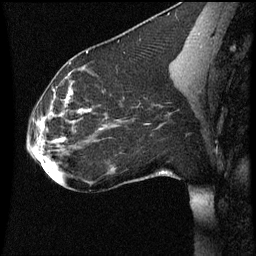
Breast MRI (dynamic contrast-enhanced), one sagittal slice; slice 28 of 60 in the series (ordered by position); dynamic contrast-enhanced series, image 2 of 3 at this slice position (ordered by acquisition); 1.5 T; TE 4.2 ms, TR 8.9 ms; 256 × 256 image matrix, field of view 200 × 200 mm. Female patient, age 35 years. From the clinical record (not read from this slice): setting: breast cancer imaged before/during neoadjuvant chemotherapy; receptor status: HER2-positive.
Annotated regions visible in this slice (semi-automatic segmentation, software-assisted and operator-edited):
- analysis volume of interest (the breast-tissue region the enhancement analysis was run in; not a lesion): bounding box [x1, y1, x2, y2] px = [25, 66, 177, 177]
- tumour enhancement mask (voxels above the 70 % enhancement threshold inside the analysis volume of interest): [36, 76, 91, 153]